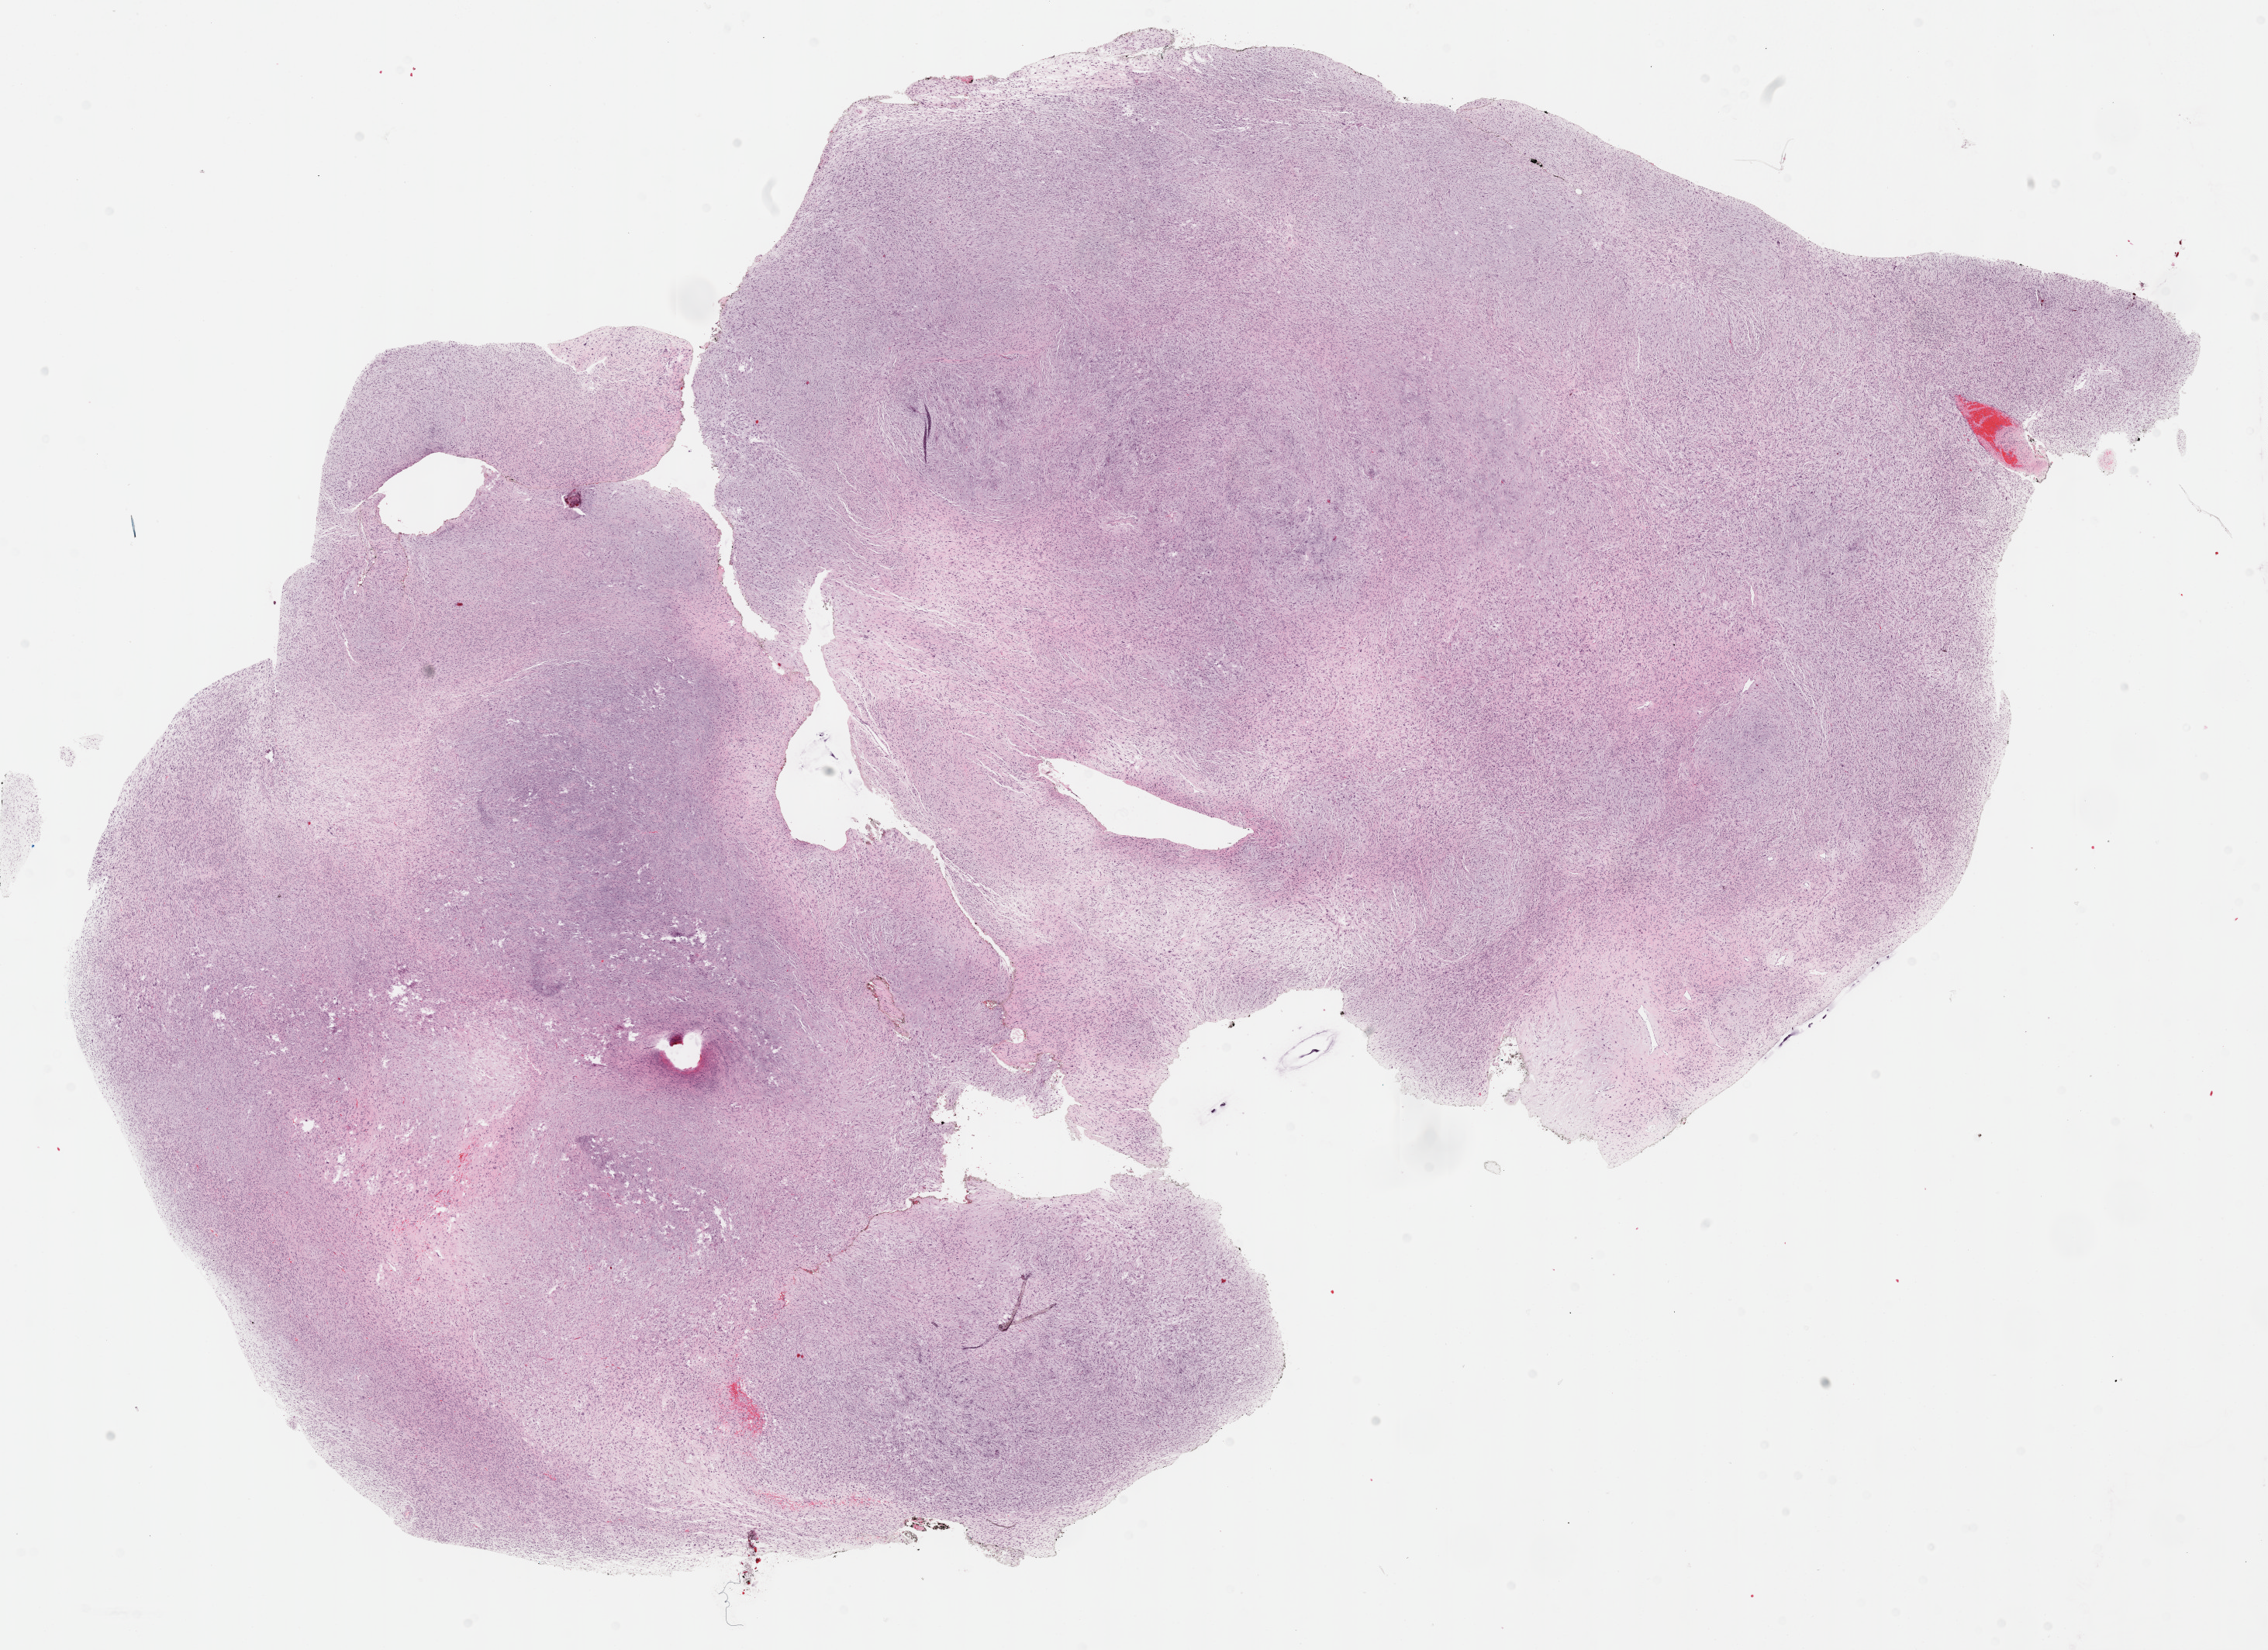
Whole-slide histology image, H&E-stained — shown as a low-resolution overview of the whole scanned area (about 23.7 x 17.2 mm); formalin-fixed paraffin-embedded (FFPE) diagnostic section; primary tumour sample from the connective, subcutaneous and other soft tissues. Patient: female, age at initial diagnosis 31 years.
Histologic diagnosis: Fibromyxosarcoma.